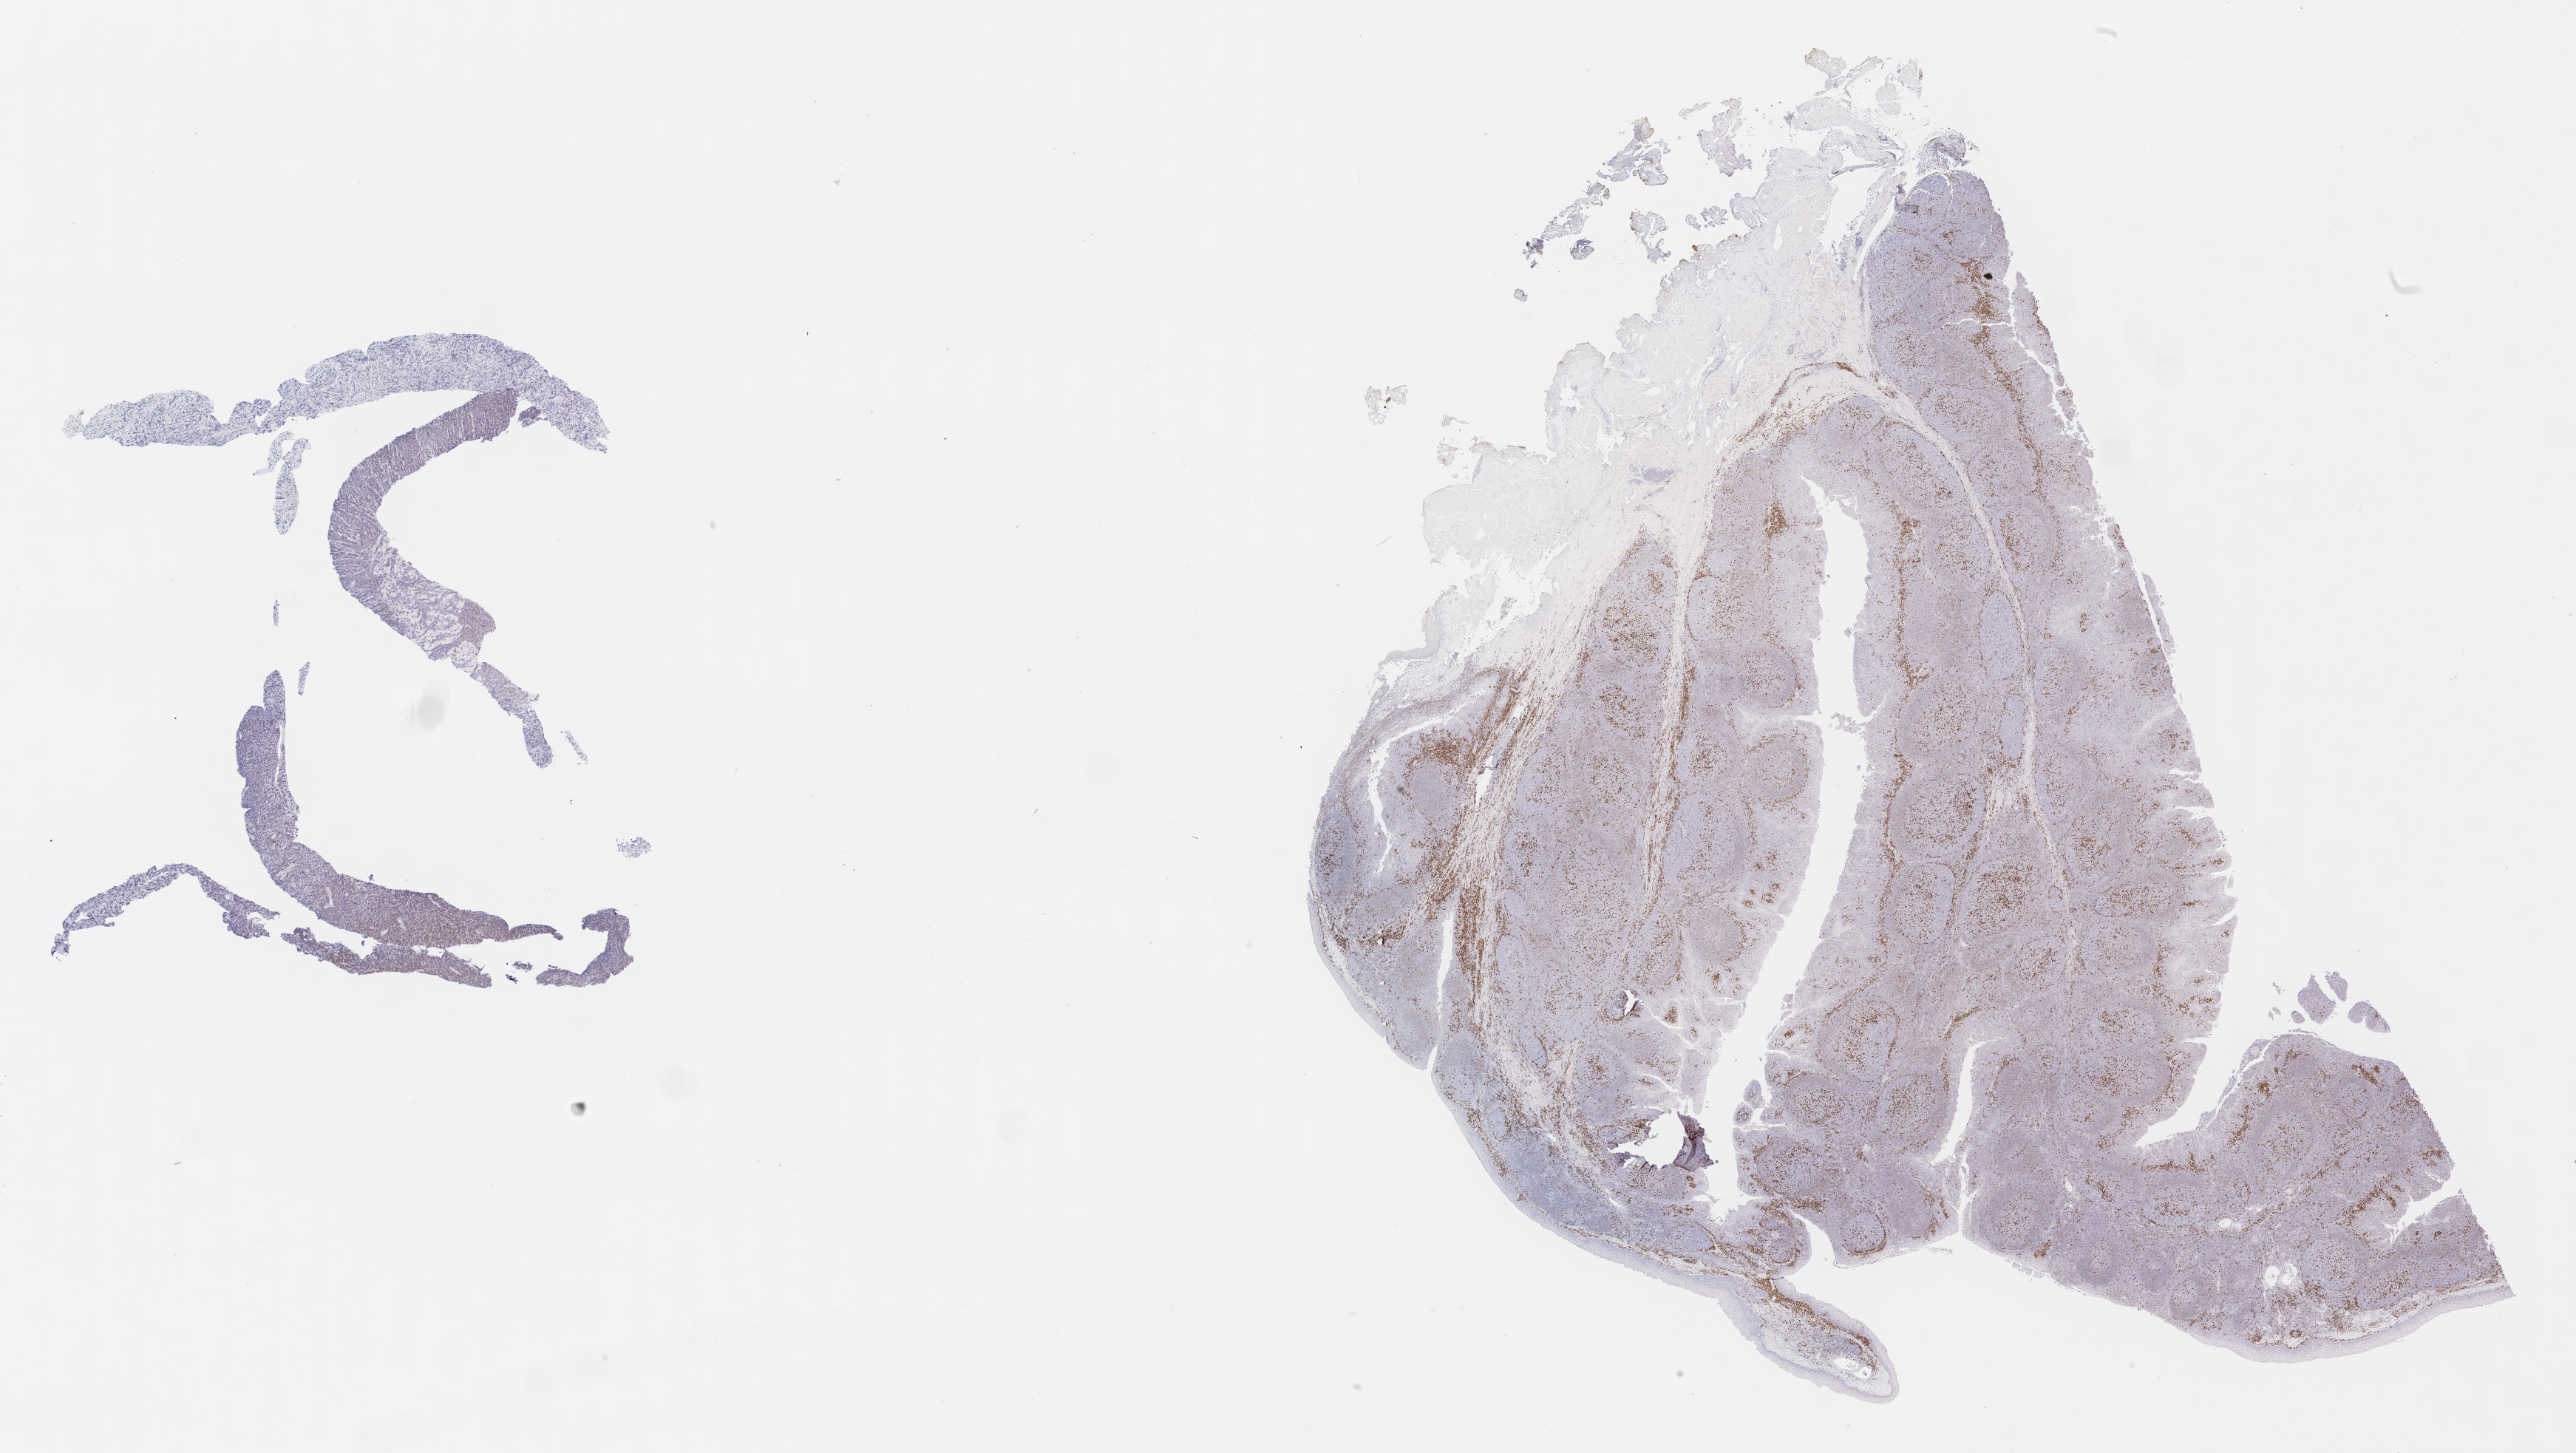
Immunohistochemistry (IHC) whole-slide image stained for IRF4/MUM1 — low-resolution overview of the scanned area, about 28.2 x 15.9 mm. Tumor tissue. Anatomic site: pleura. Male patient; age at initial diagnosis 2 years.
Diagnosis: Diffuse large B-cell lymphoma, NOS.